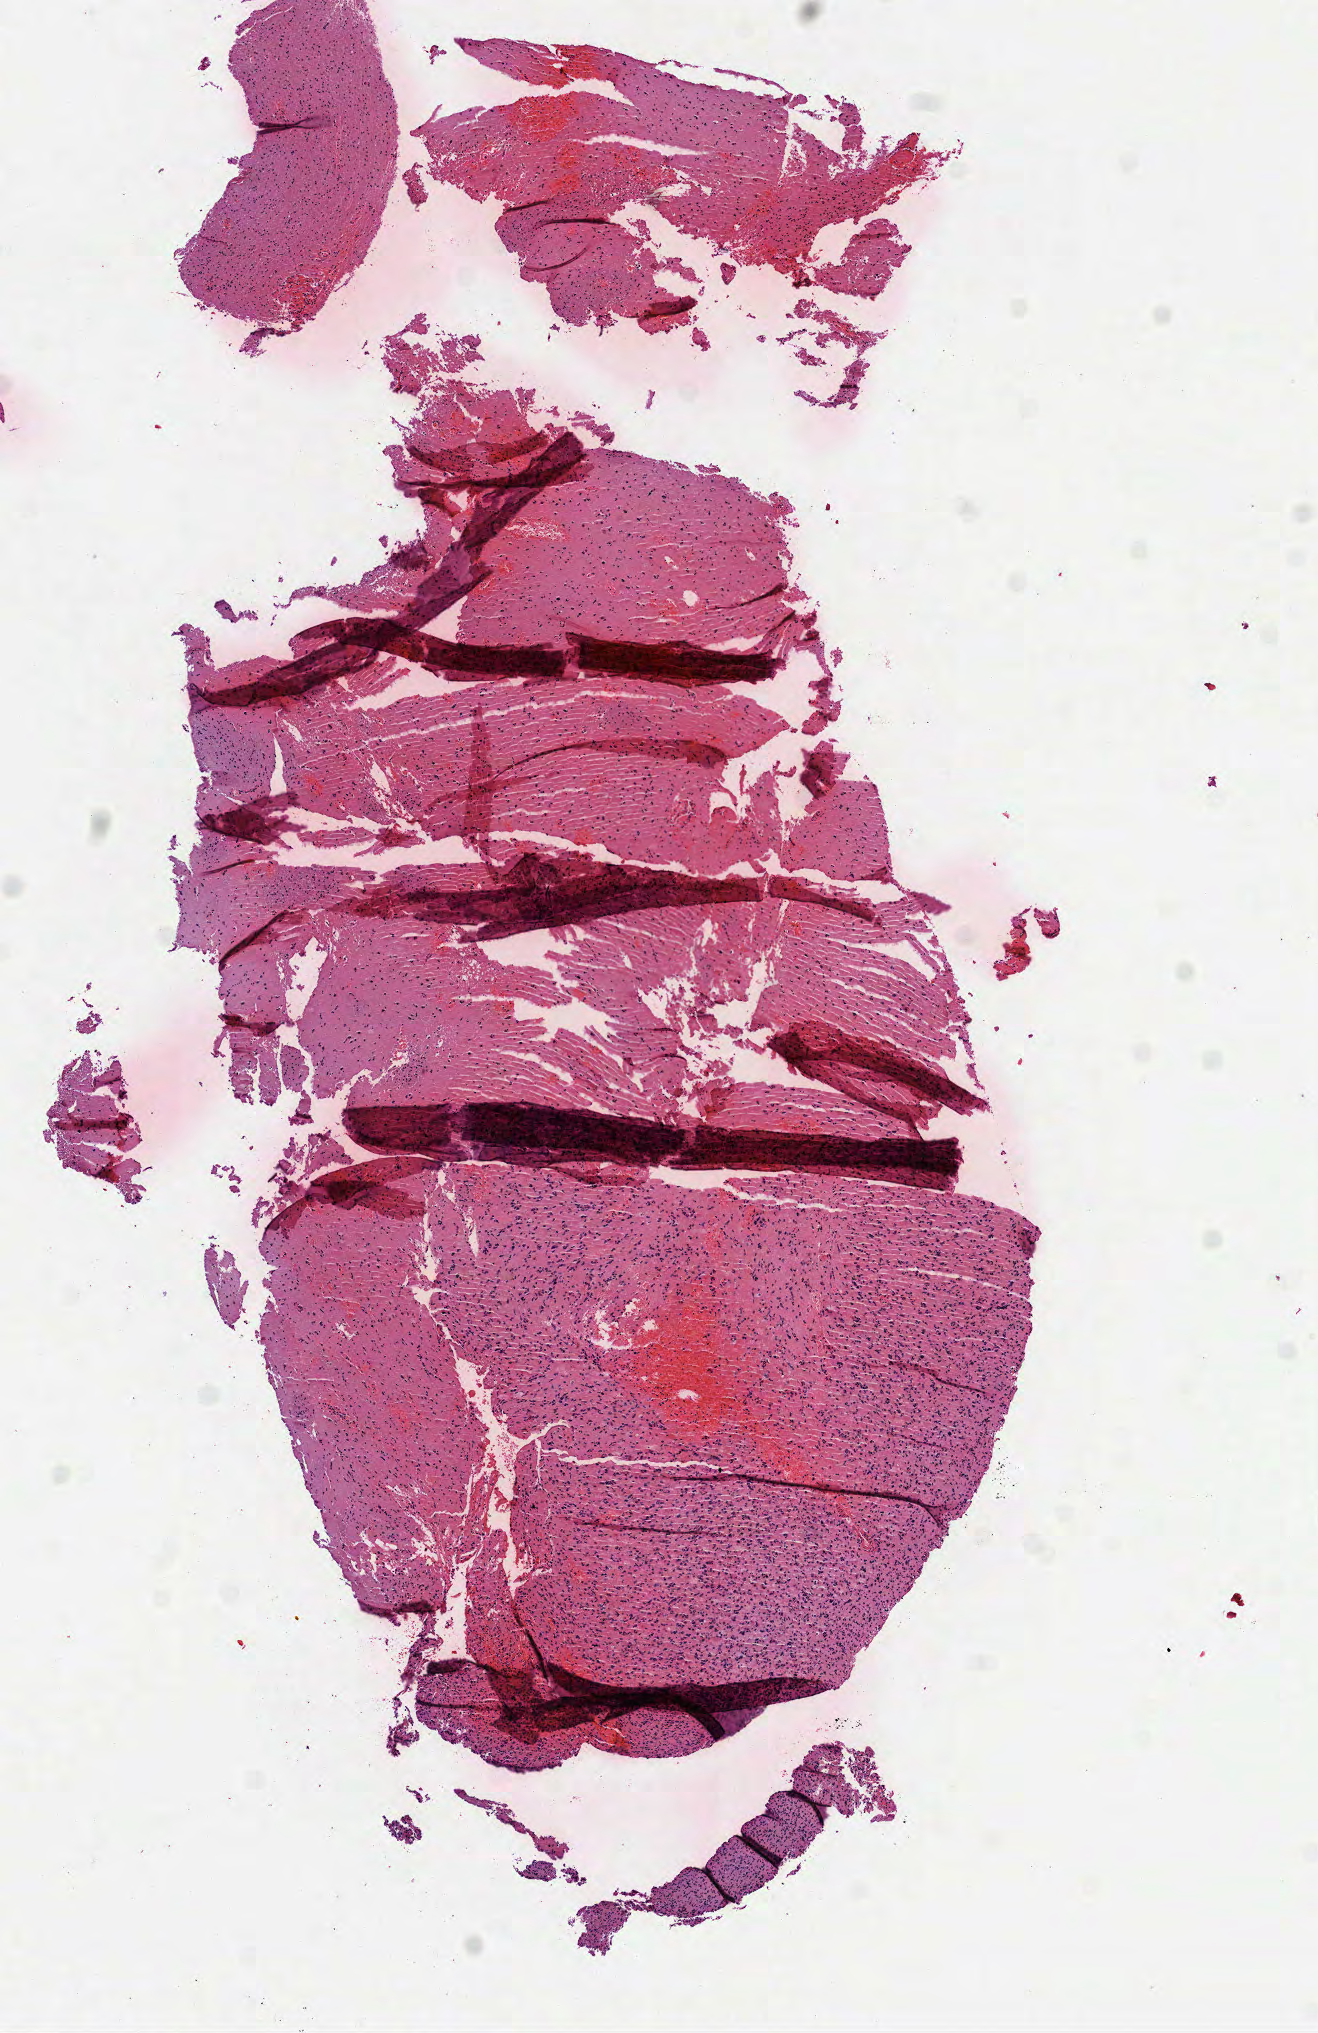
Digitized Hematoxylin and eosin (H&E) stained tissue section (whole slide) — low-resolution overview of the scanned area, about 5.3 x 8.2 mm (from a 40x scan), FFPE section, sample: primary tumour, brain. Patient: male, age at initial diagnosis 67 years. Histologic grade: G3 (poorly differentiated).
- pathologic diagnosis: Astrocytoma, anaplastic